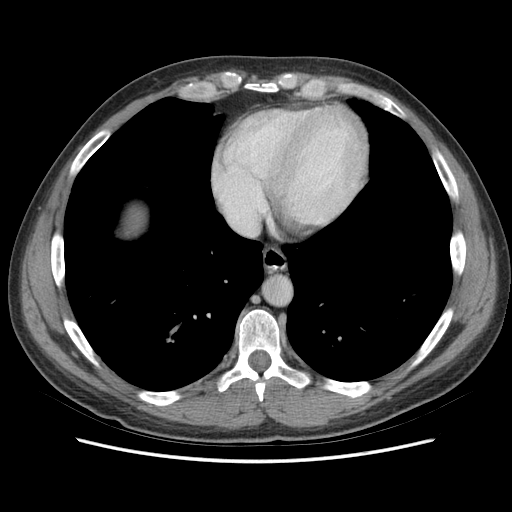
Contrast-enhanced abdominal CT (liver protocol), one axial slice. Slice 71 of 73 in the series (ordered by position). Reconstruction kernel STANDARD. 140 kVp. Soft-tissue window (W 400 / L 40 HU). 512 × 512 image matrix, field of view 360 × 360 mm. Case-level facts recorded for this patient, not image findings: diagnosis: hepatocellular carcinoma (patient treated with transarterial chemoembolisation; whether this scan precedes or follows treatment is not stated here); TNM stage (as recorded): Stage-IIIA; Child-Pugh class: A; tumour nodularity: multinodular; tumour size: 6.6 cm.
Structures marked on this image (semi-automatically segmented with operator editing):
- abdominal aorta: bounding box (x1, y1, x2, y2) in pixels: (264, 278, 290, 305)
- liver parenchyma outside the tumour (the mass and vessels are separate outlines, so this box may not span the whole liver): (126, 208, 142, 230)